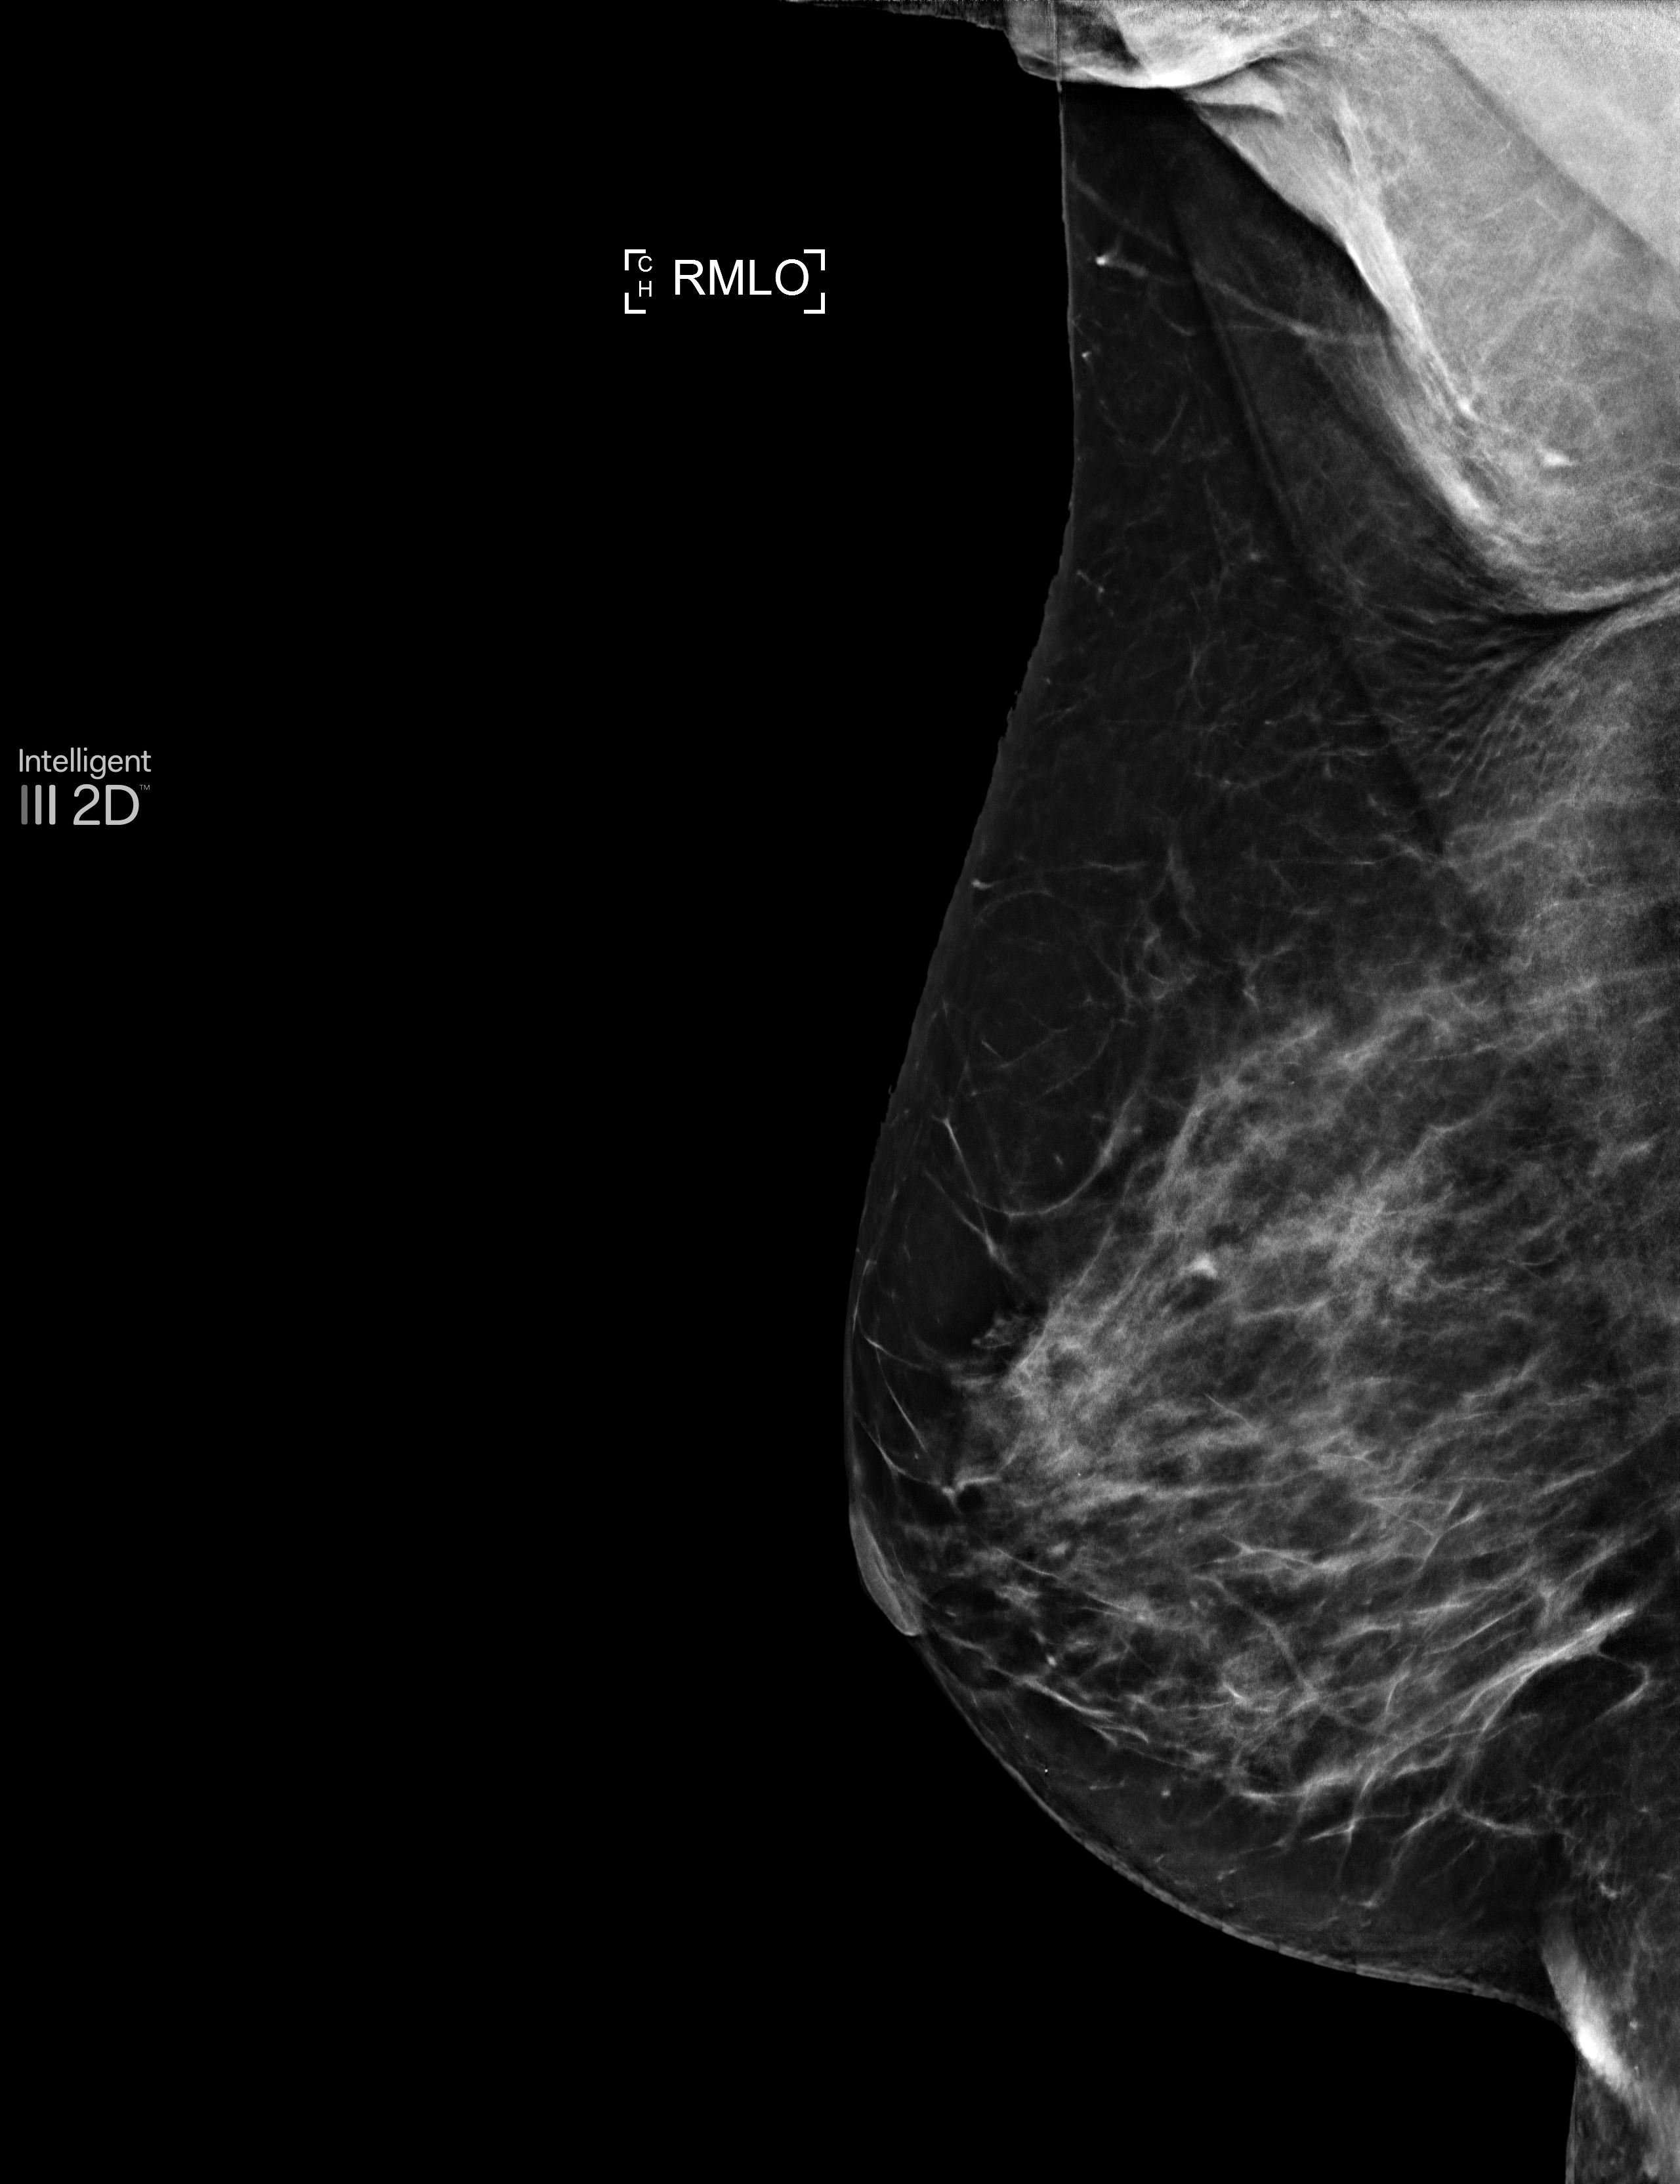
Annual screening mammography examination; compressed breast thickness 65 mm. Patient aged 60 years (female).
Image type: synthesized 2-D view from tomosynthesis. Breast: right. Projection: MLO view.